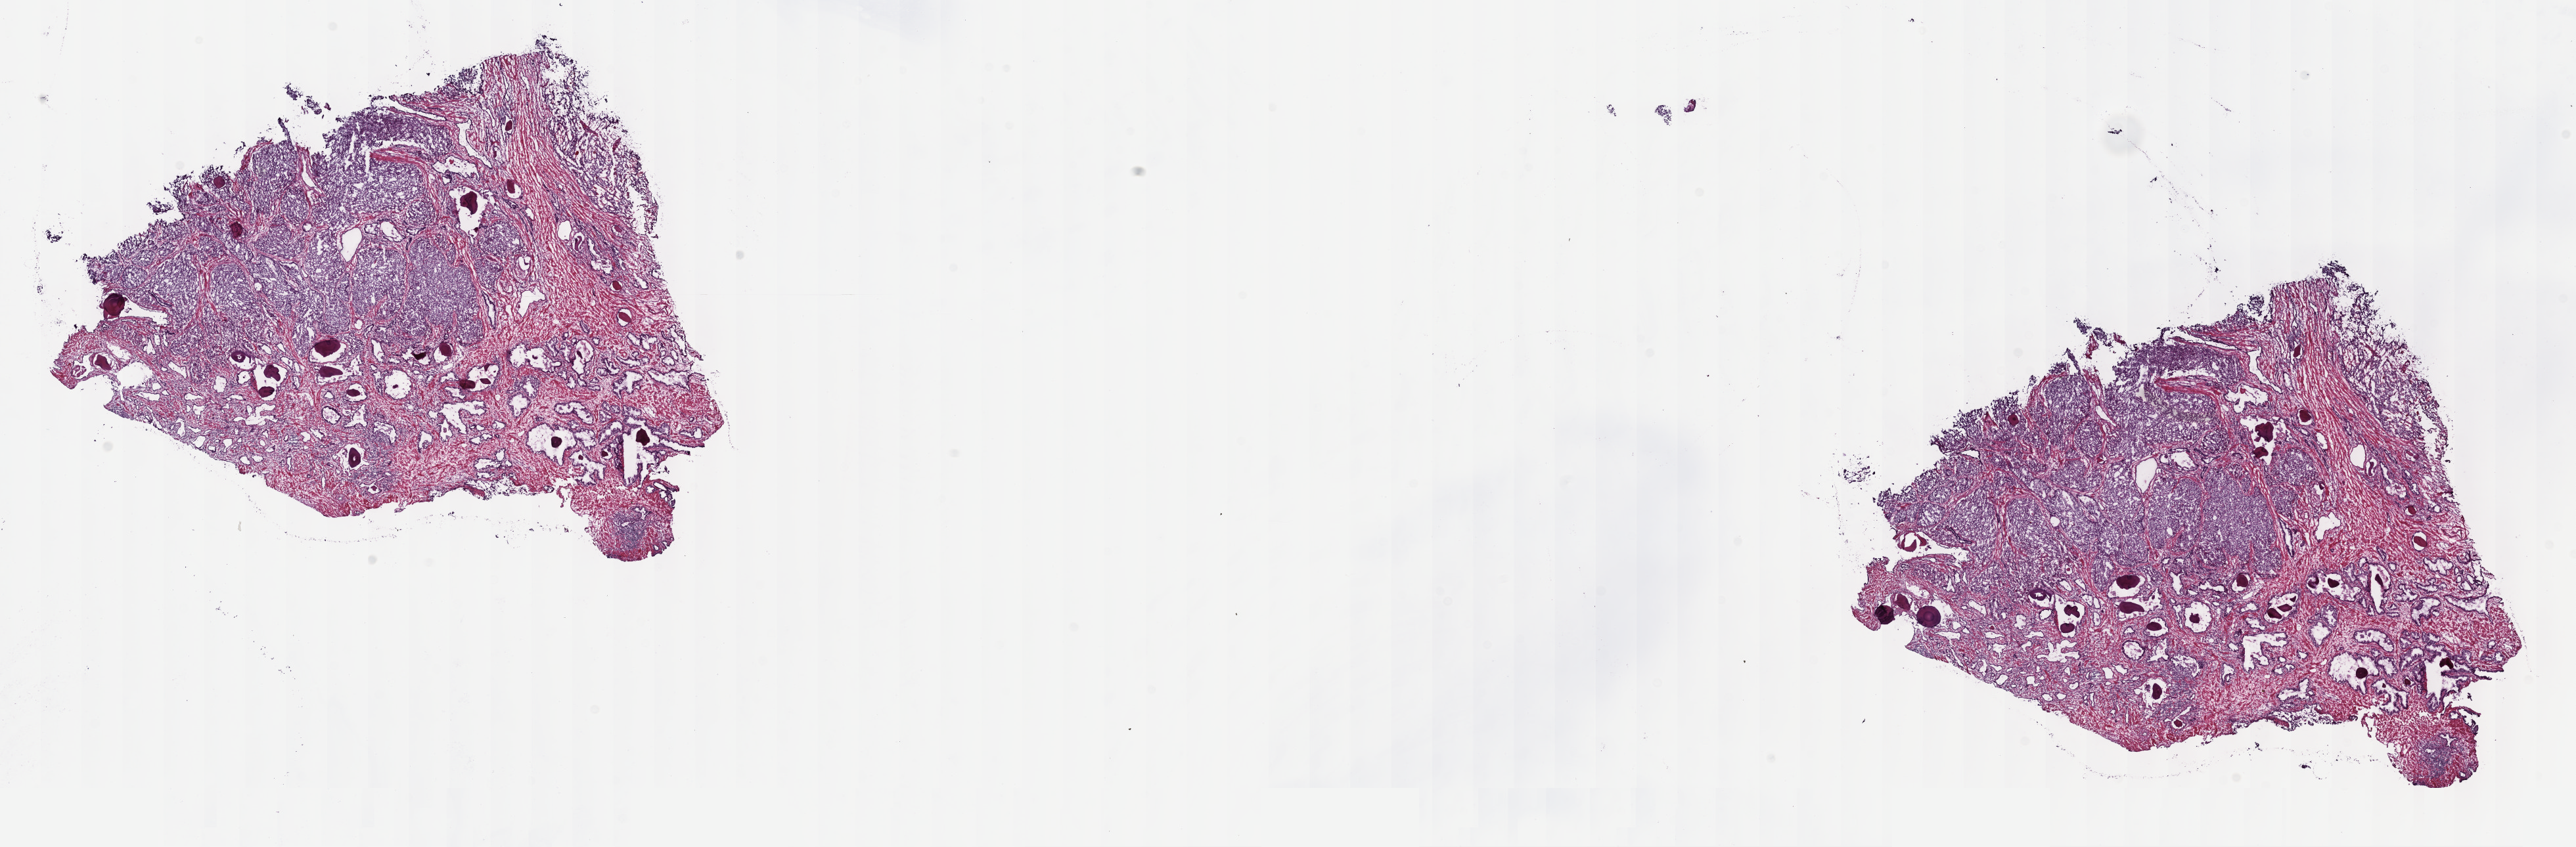
H&E-stained whole-slide image — a low-resolution overview of the entire scanned area, about 31.7 x 10.4 mm (slide scanned at 40x), frozen section from the top of the tissue portion, prostate, primary tumour sample. Male, age 65 years at initial diagnosis. Gleason score: 9 (4+5). Slide review estimates, as recorded: tumour cells 50%, tumour nuclei 60%, normal cells 50%, stromal cells 0%, necrosis 0%. Infiltration values recorded for this section: lymphocyte infiltration 0%, monocyte infiltration 0%, neutrophil infiltration 0%.
- pathologic diagnosis: Adenocarcinoma, NOS
- laterality: bilateral